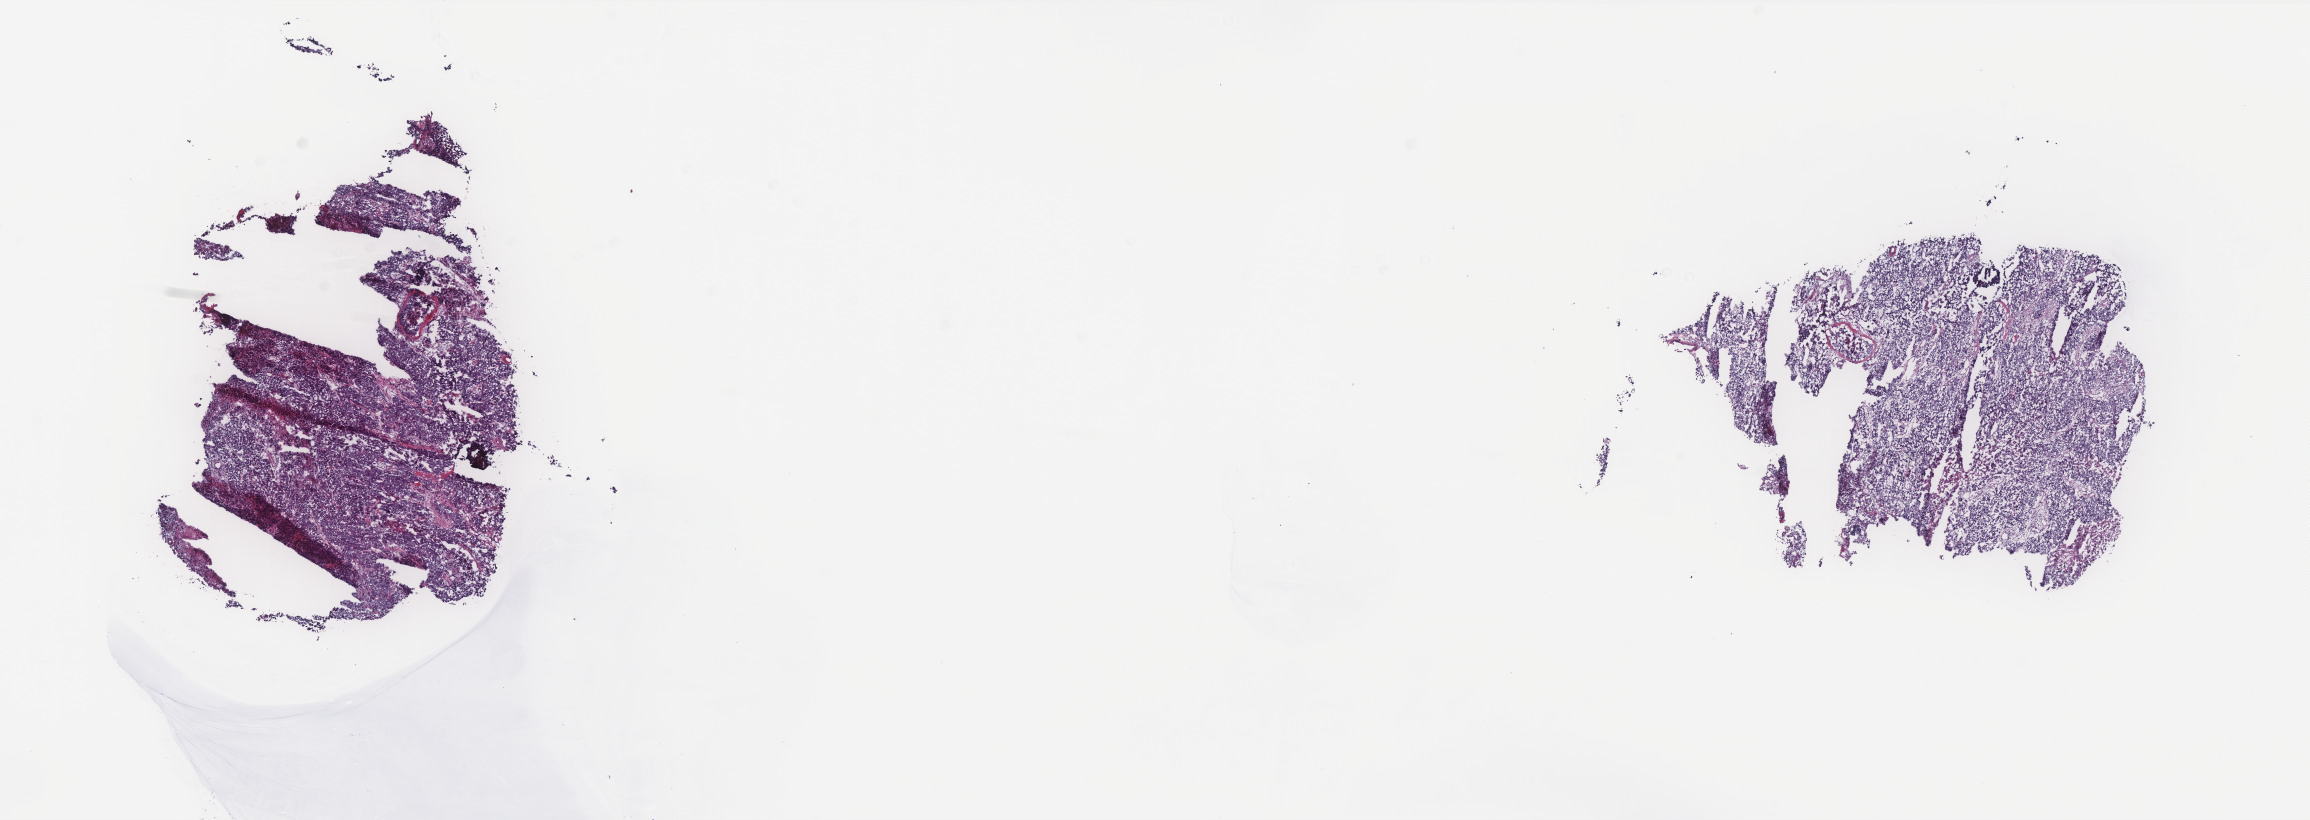
H&E whole-slide image, whole scanned area (about 18.5 x 6.6 mm) shown as a low-resolution overview; frozen section; cervix, primary tumour sample. Female, age 55 years at initial diagnosis. Histologic grade: G3 (poorly differentiated). Composition of this section per pathologist review: tumour cells 85%, tumour nuclei 95%, normal cells 0%, stromal cells 5%, necrosis 10%. Infiltration values recorded for this section: lymphocyte infiltration 3%, monocyte infiltration 5%, neutrophil infiltration 2%.
FIGO stage: IIB. Diagnosis: Squamous cell carcinoma, NOS (cervix uteri).